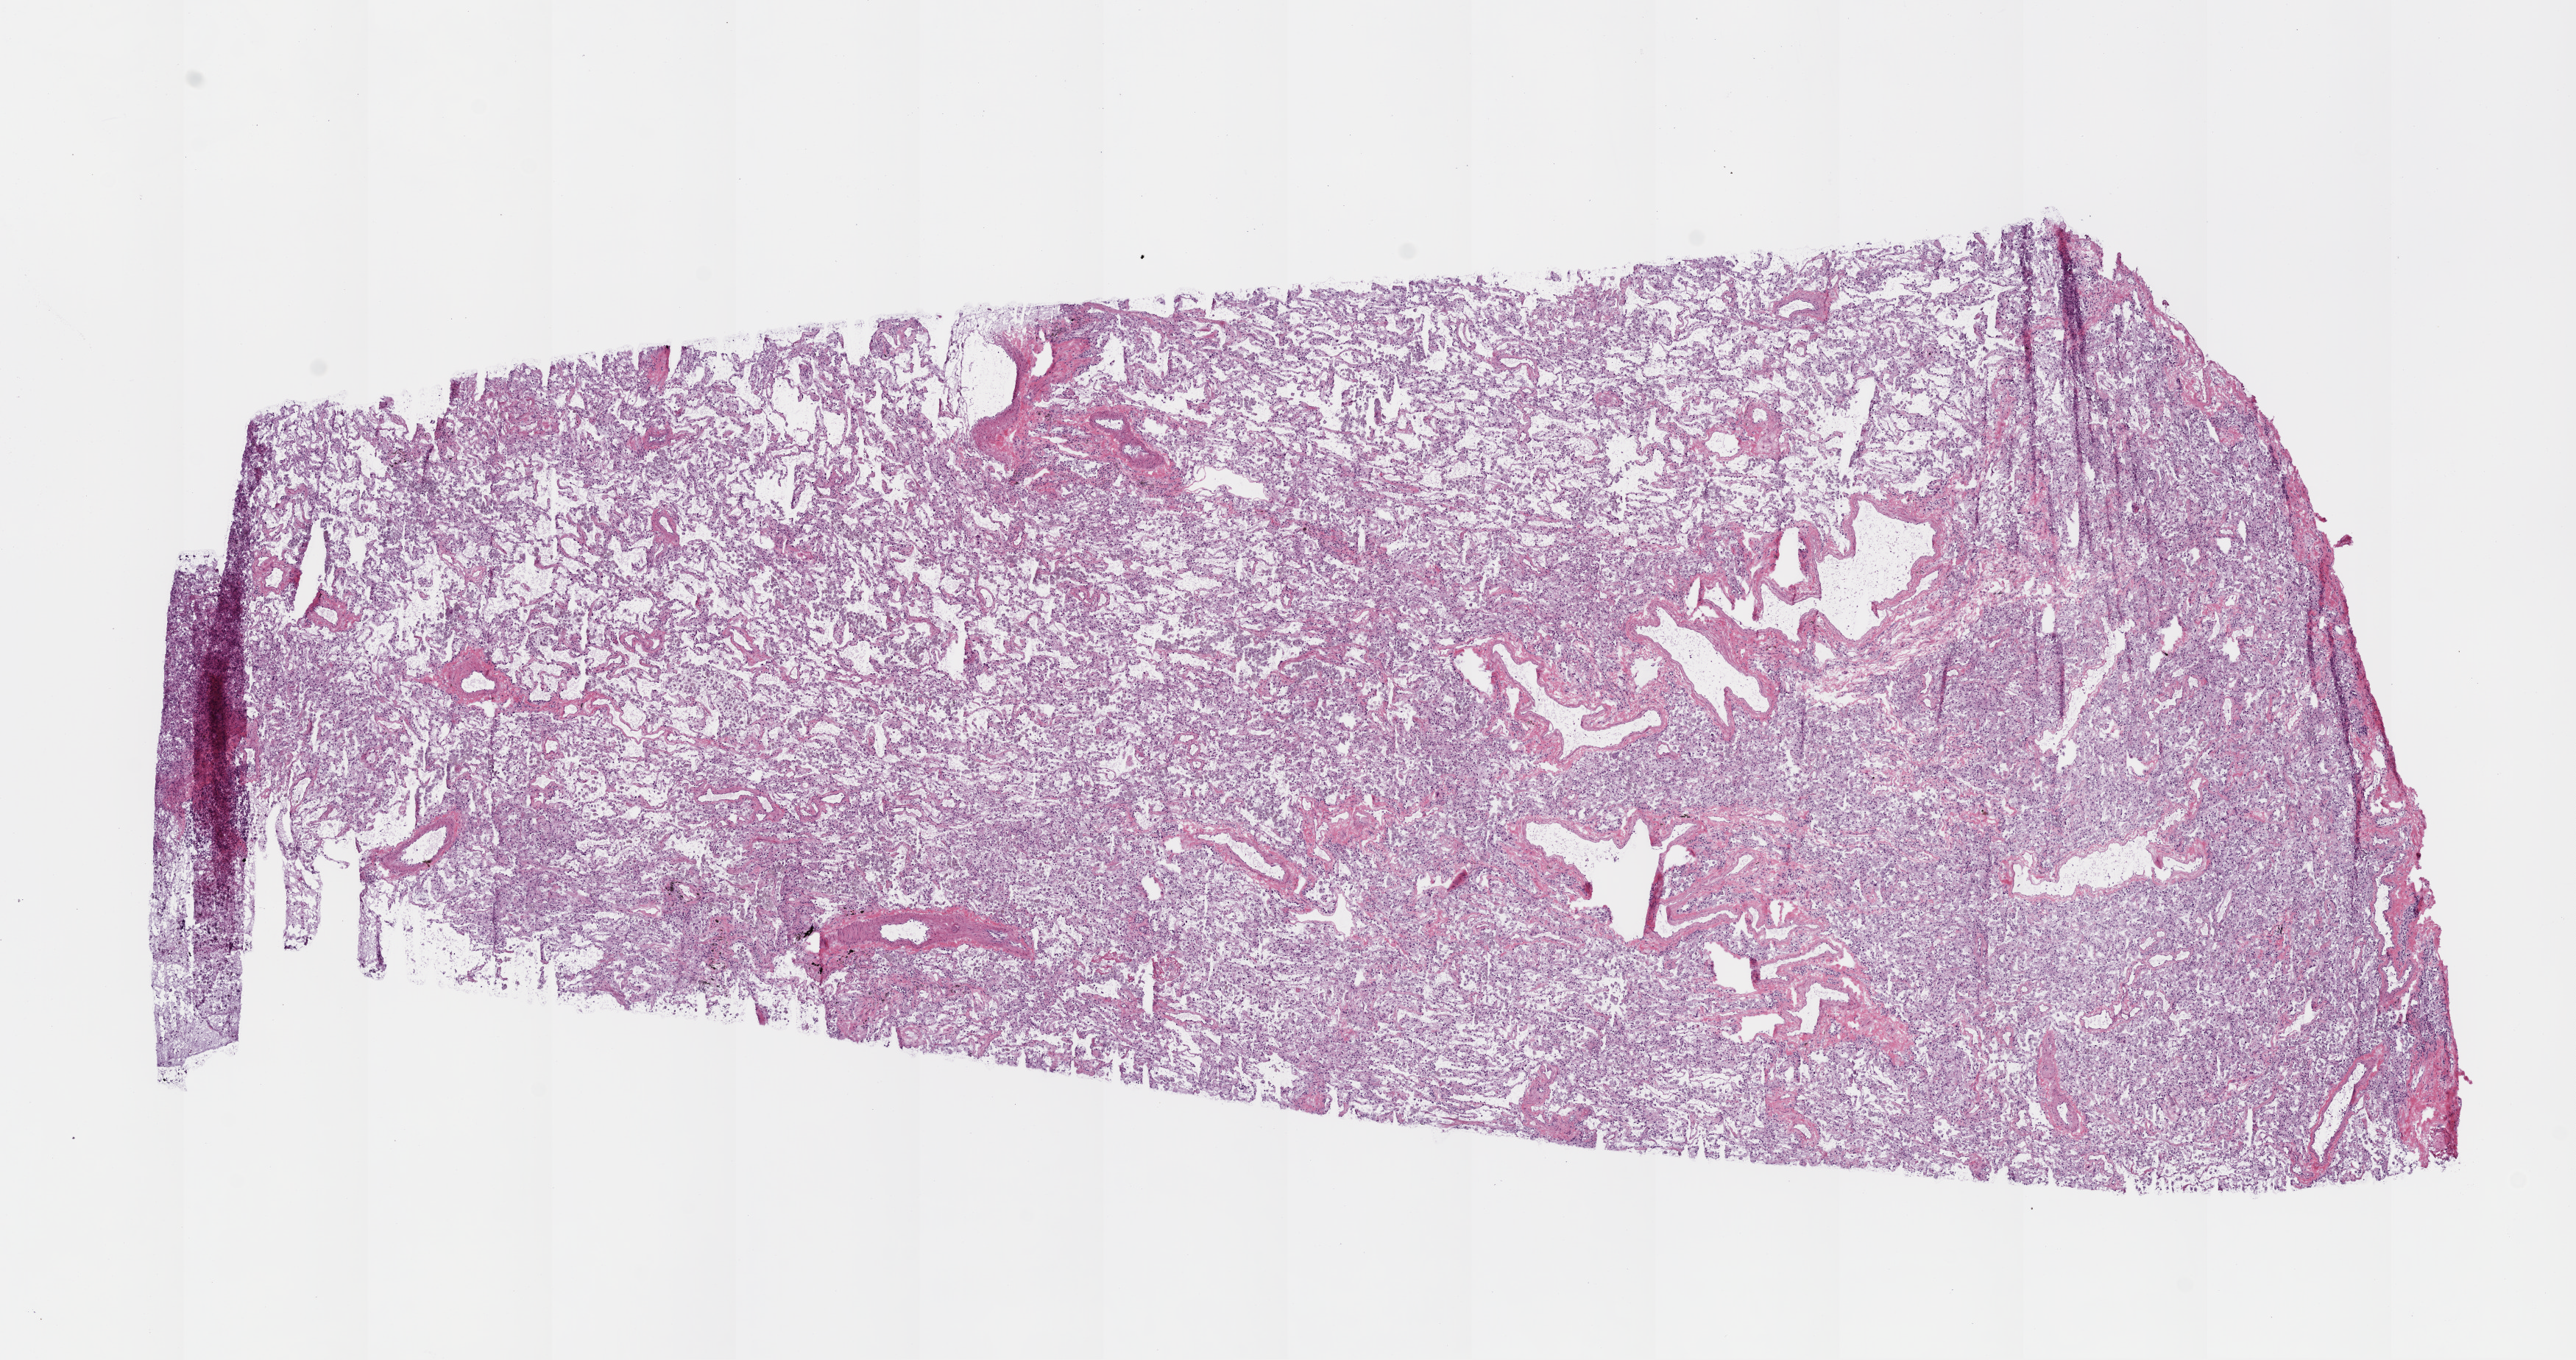
Digitized H&E-stained tissue section (whole slide), whole scanned area (about 14.0 x 7.4 mm, acquisition: 20x scan) shown as a low-resolution overview. Frozen section from the top of the tissue portion. Sample: solid tissue normal (non-tumour tissue), lung. Male patient; age at initial diagnosis 52 years.
This section: solid tissue normal (non-tumour) sample from the same patient. Patient diagnosis: Squamous cell carcinoma, NOS (lower lobe, lung).